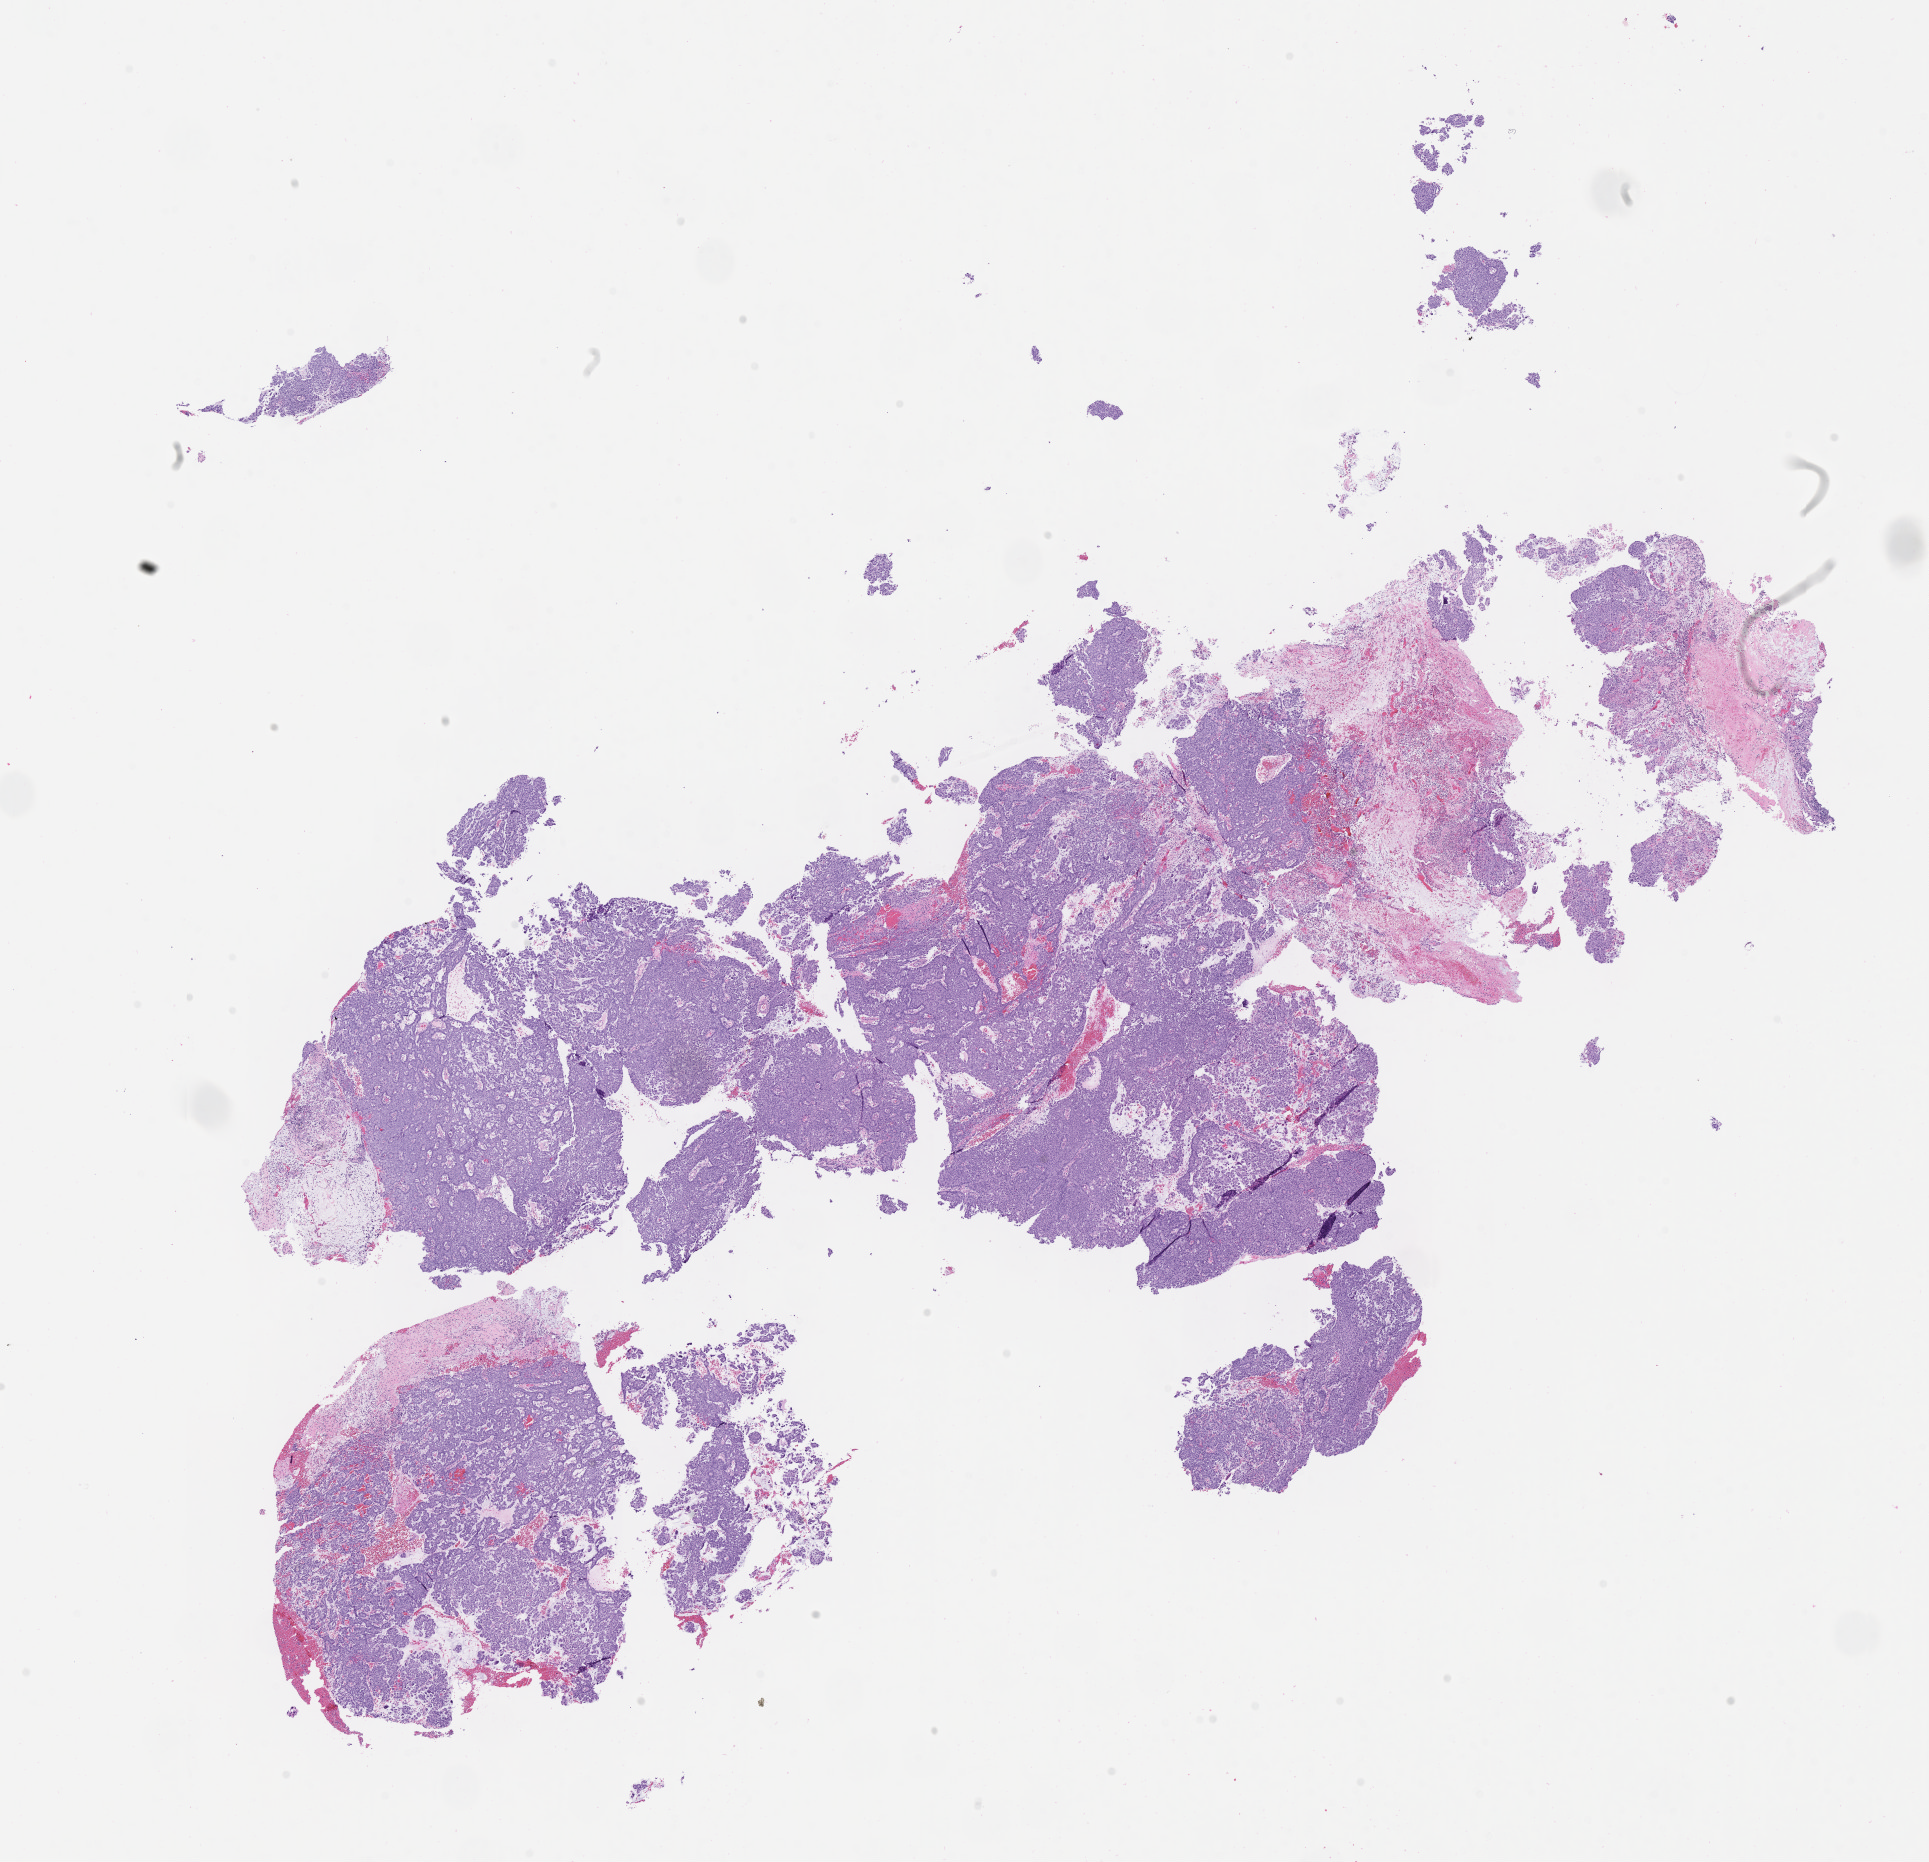
Whole-slide image, haematoxylin and eosin stain, shown as a low-resolution overview of the whole scanned area (about 15.6 x 15.1 mm). Tumor tissue. Anatomic site: cervix. Patient female; aged 47.
* diagnosis: Adenocarcinoma, NOS